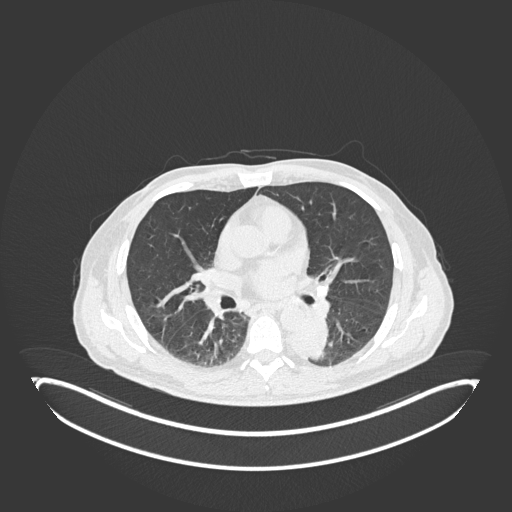
Chest CT, one axial slice; slice 105 of 251 in the series (ordered by position); reconstruction kernel B30f; lung window (W 1500 / L -600 HU); 1 mm slice thickness; 512 × 512 image matrix. Male patient, age 72 years. Case-level facts recorded for this patient, not image findings: clinical TNM (as recorded): T2b N0 M1.
Outlined on this slice (bounding box drawn by a radiologist):
- lung tumour (recorded histology: adenocarcinoma): bounding box (x1, y1, x2, y2) in pixels: (280, 308, 330, 363)